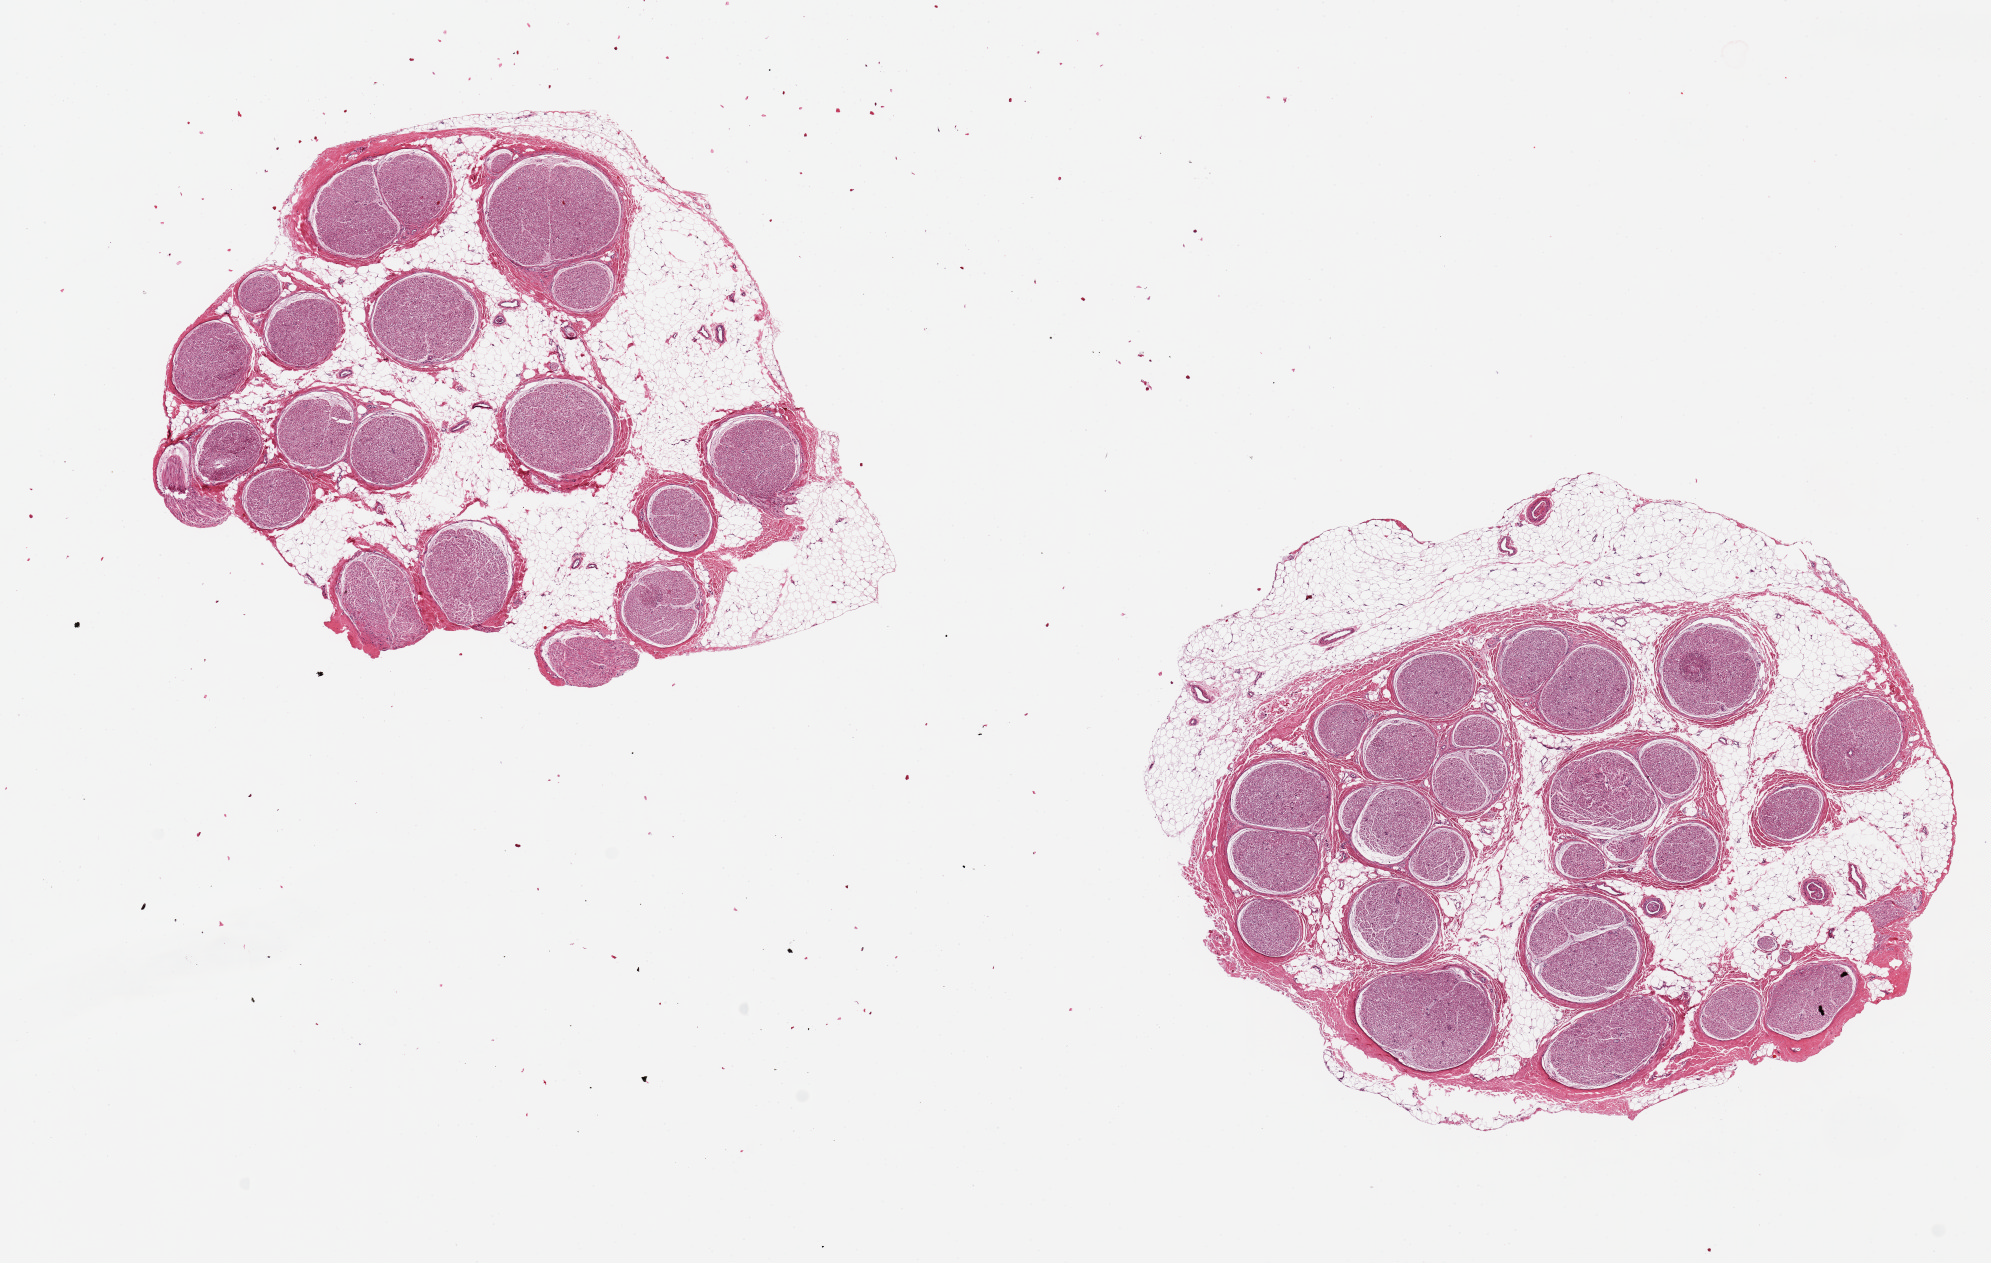
Digitized hematoxylin and eosin (H&E)-stained section, low-resolution overview of the scanned area, about 15.8 x 10.0 mm; PAXgene-fixed paraffin-embedded (PFPE) section; target tissue: tibial nerve; donor tissue sample. Male donor.
Reviewer comment on this tissue sample: 2 pieces ~5mm d.